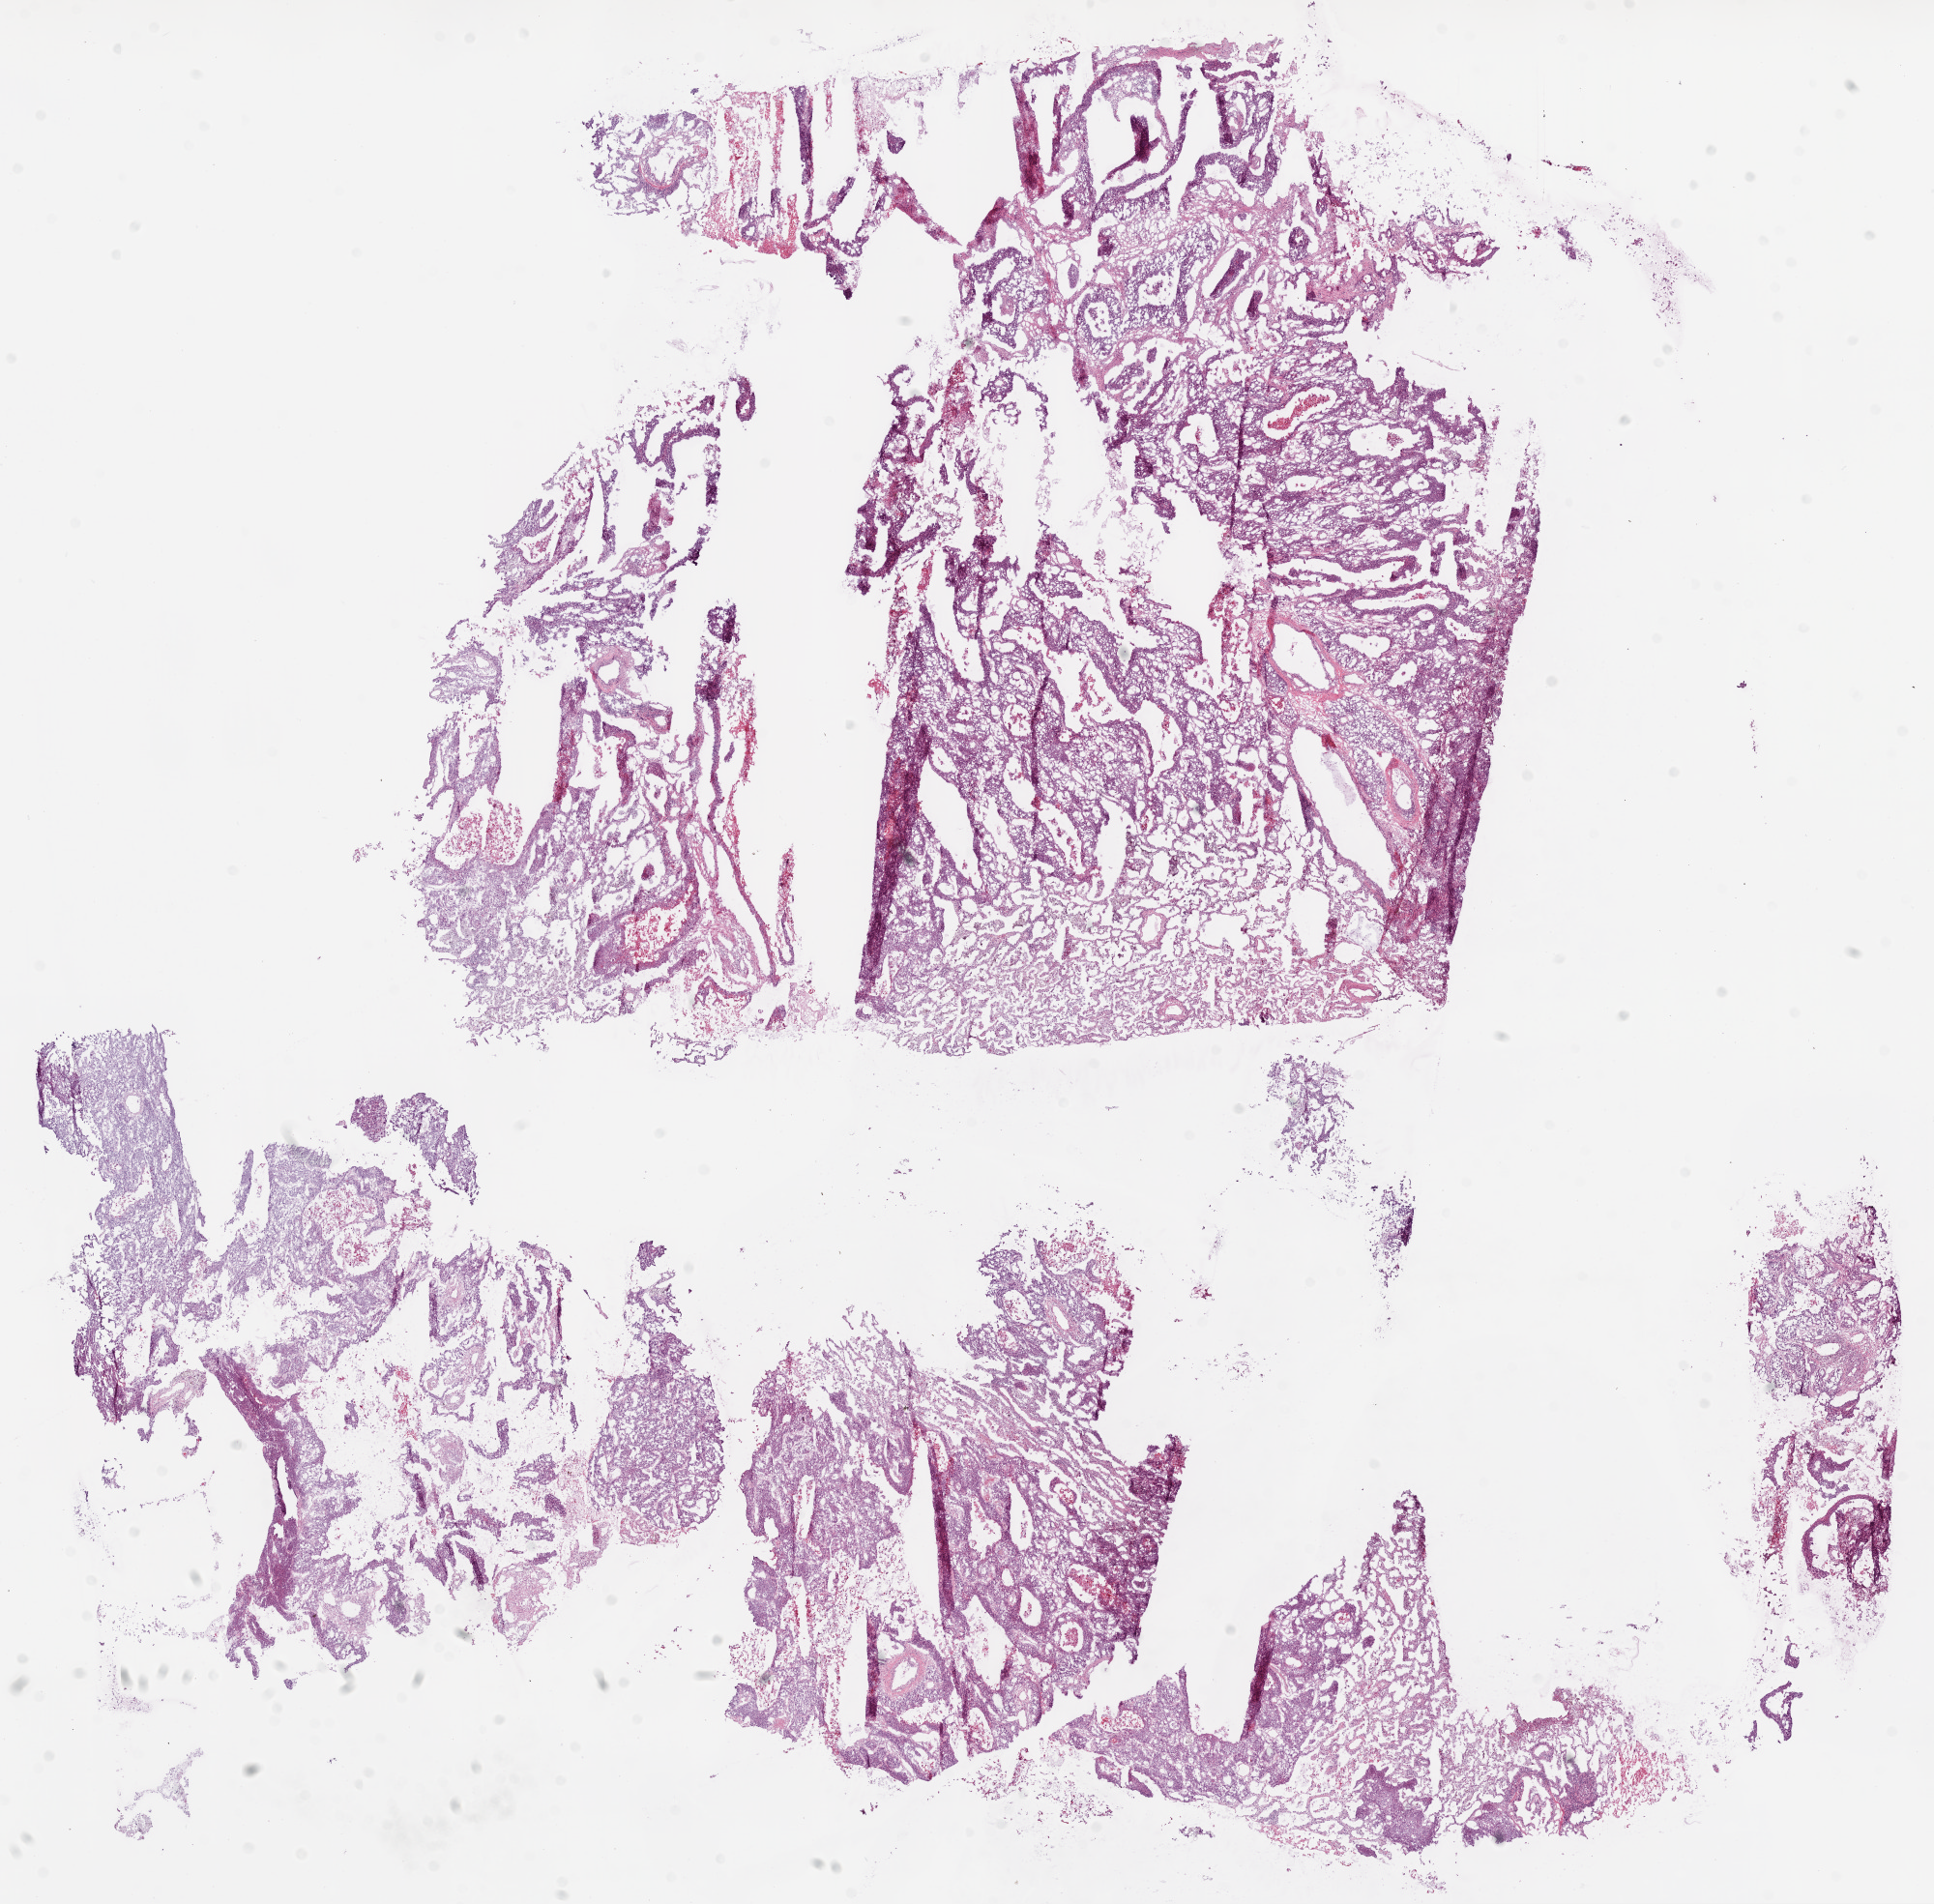
H&E-stained whole-slide image, a low-resolution overview of the entire scanned area, about 16.0 x 15.8 mm (from a 20x scan). Frozen section from the top of the tissue portion. Lung, primary tumour sample. Patient: male, age at initial diagnosis 65 years. Composition of this section per pathologist review: tumour cells 70%, tumour nuclei 75%, normal cells 10%, stromal cells 15%, necrosis 5%.
Histologic diagnosis: Squamous cell carcinoma, NOS (lower lobe, lung). Laterality: left. AJCC pathologic stage: IIA.